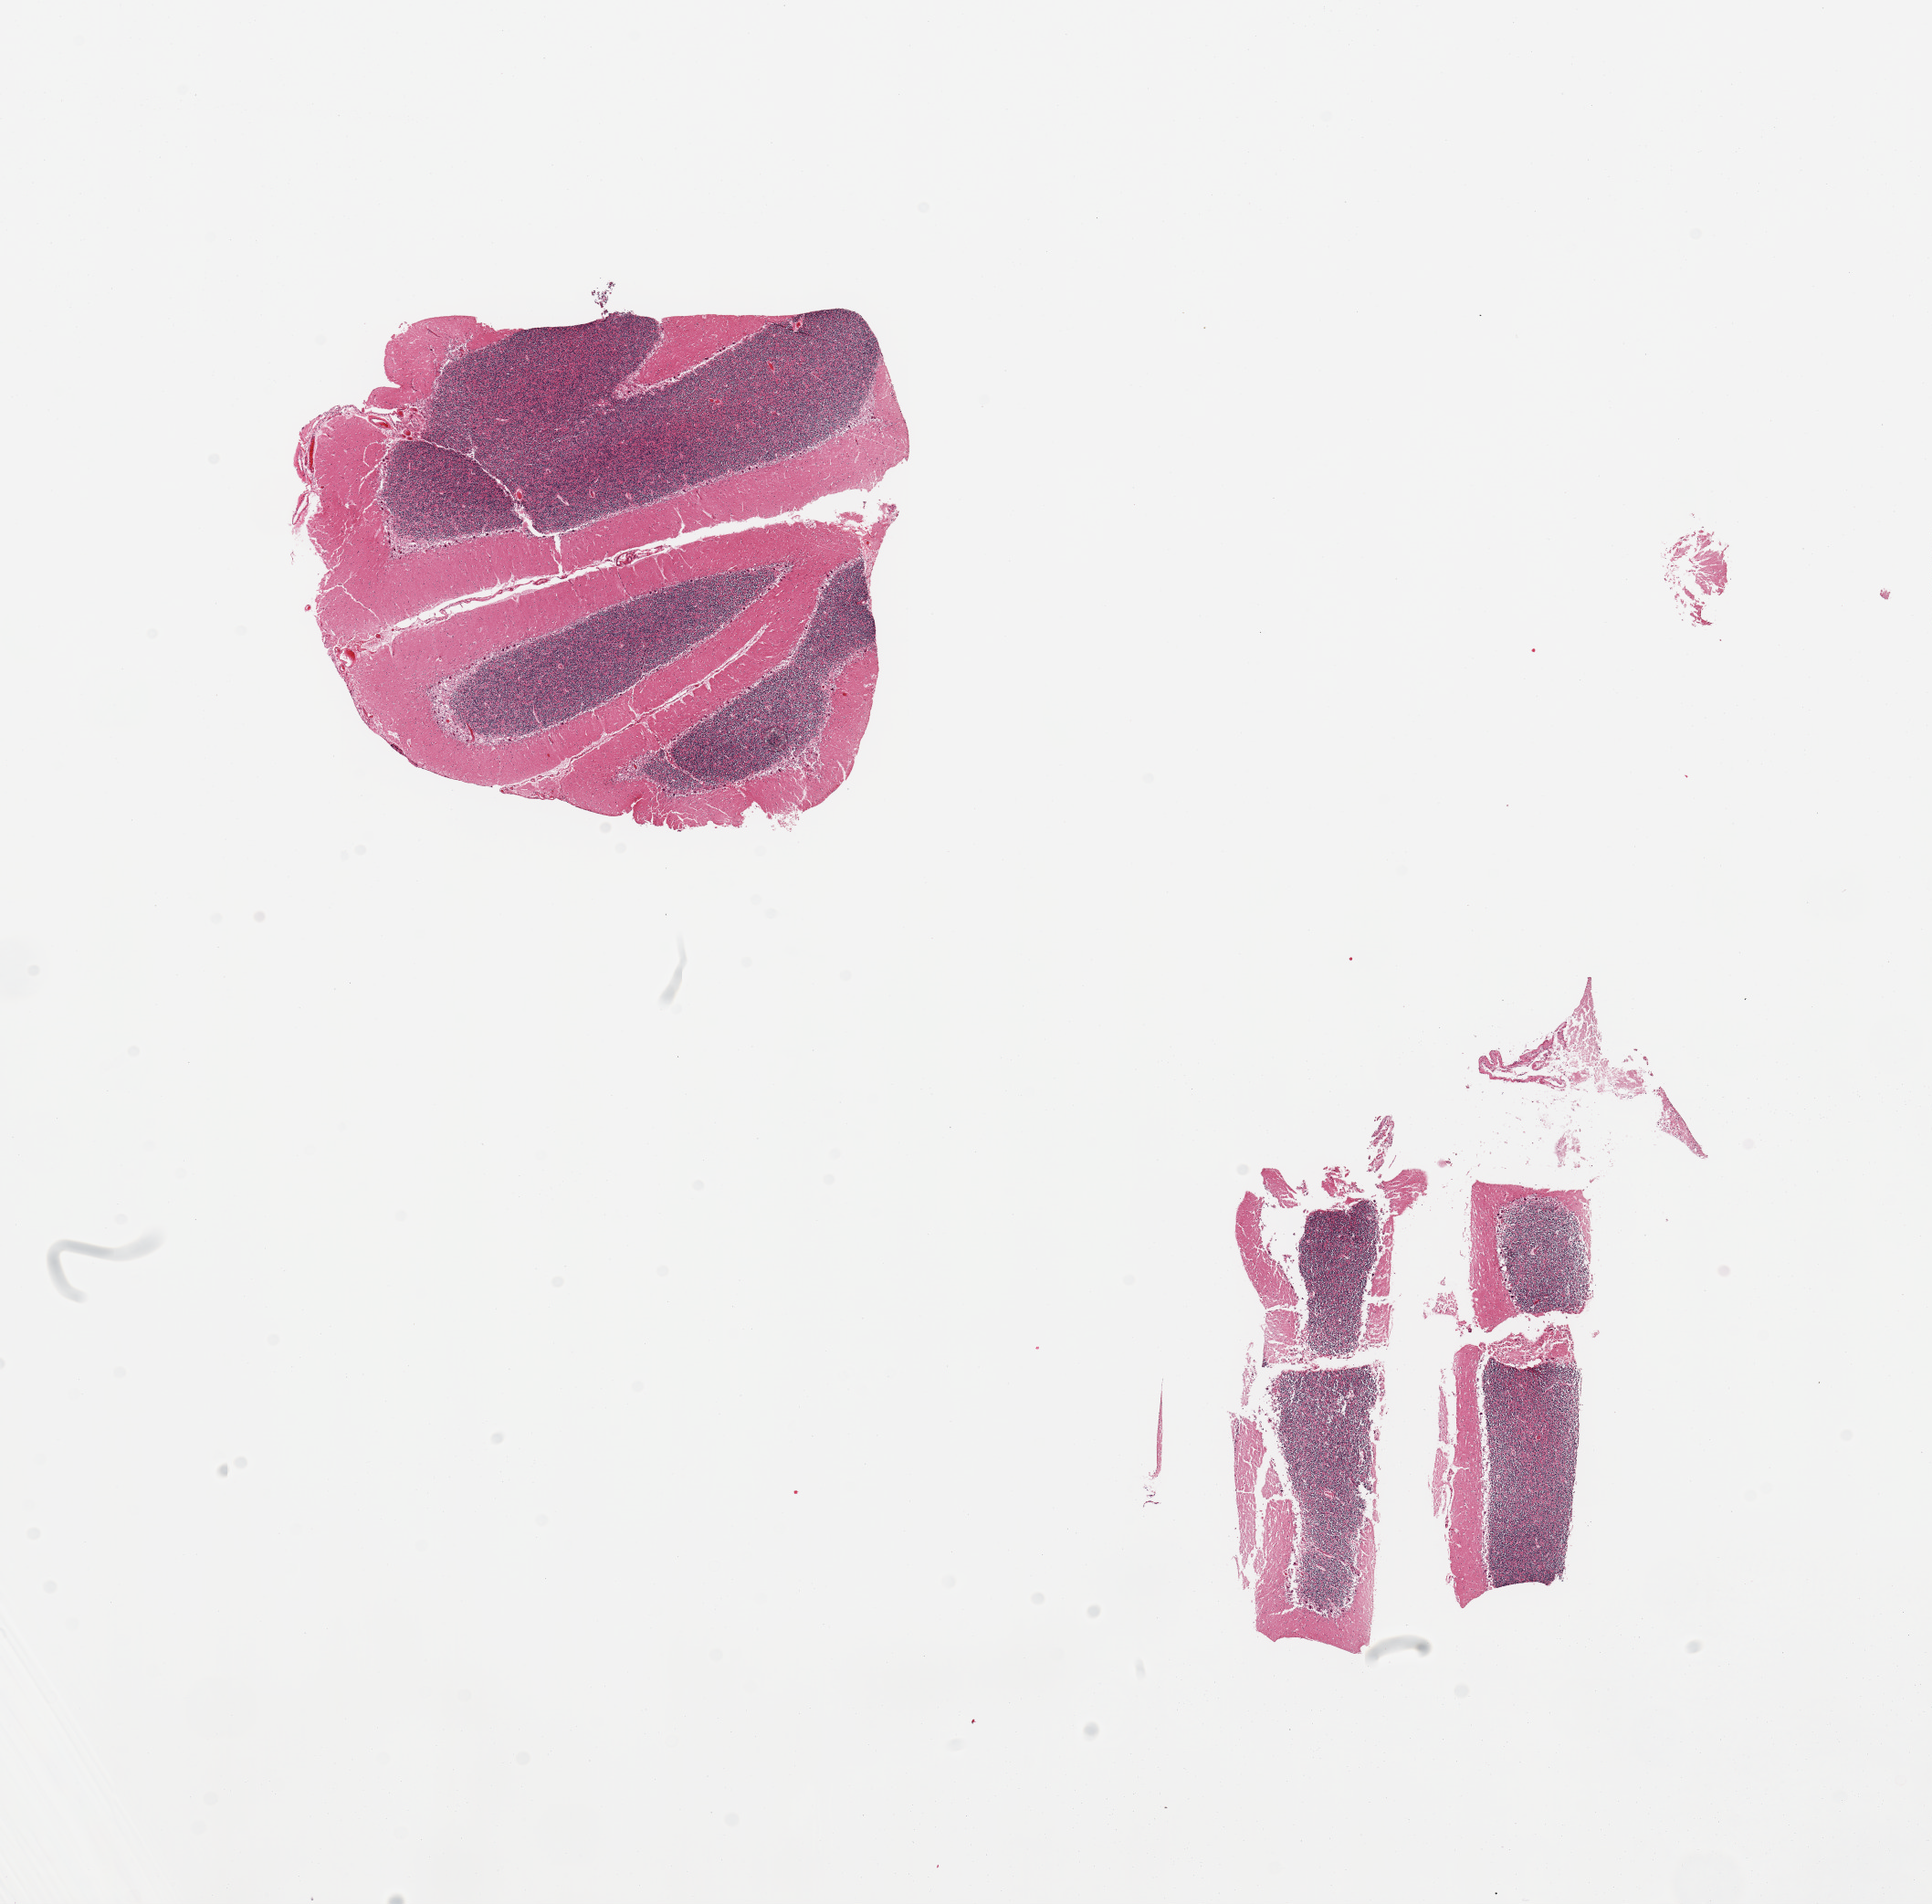
Whole-slide image, hematoxylin and eosin (H&E) stain — a low-resolution overview of the entire scanned area, about 16.7 x 16.5 mm (slide scanned at 20x); PAXgene-fixed paraffin-embedded (PFPE) section; sampled site (target tissue): cerebellum; tissue donor sample. Donor: male.
Pathologist's review note for this sample: 2 pieces, cerebellum, no abnormalities.